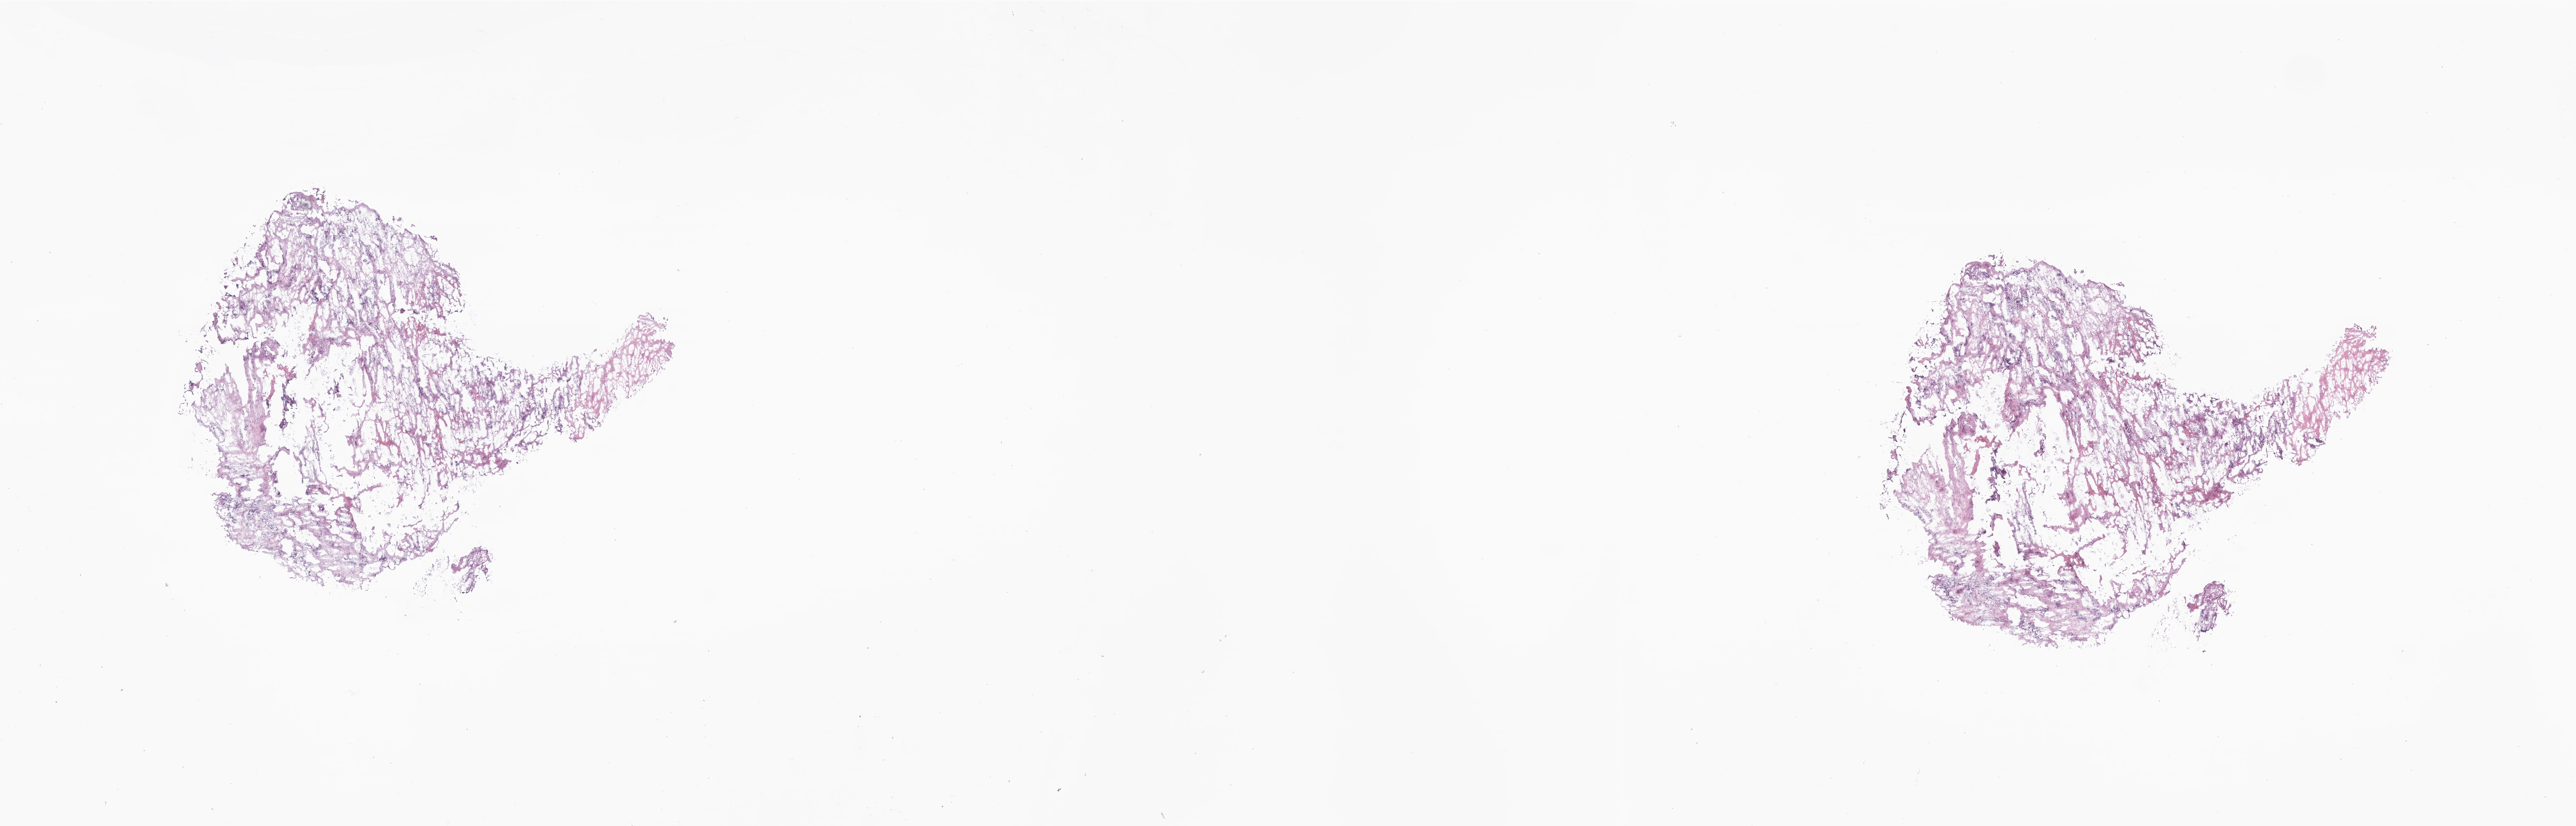
Digitized H&E-stained section of tumor tissue from the mouth, a low-resolution overview of the entire scanned area, about 27.3 x 8.8 mm, frozen section (OCT-embedded). Patient male; age 377 days (about 1.0 years).
Diagnosis: Neuroblastoma, NOS.